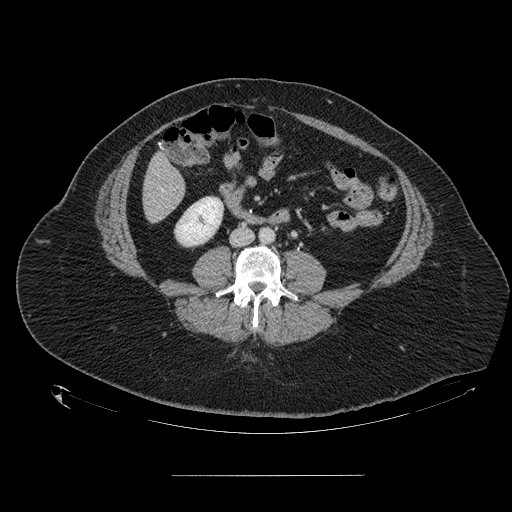
Contrast-enhanced abdominal CT, one axial slice; position 23 of 164 along the scan axis; 120 kVp; intravenous contrast given; soft-tissue window (W 400 / L 40 HU); 2.5 mm slice thickness; 512 × 512 image matrix, field of view 495 × 495 mm. Female patient, age 52 years. Case-level facts recorded for this patient, not image findings: diagnosis: colorectal cancer liver metastases, imaged before liver resection; multiple liver metastases: yes; largest metastasis: 3.5 cm.
Structures marked on this image (outlined manually by an expert reader):
- liver: box from (x=144, y=155) to (x=185, y=222) px